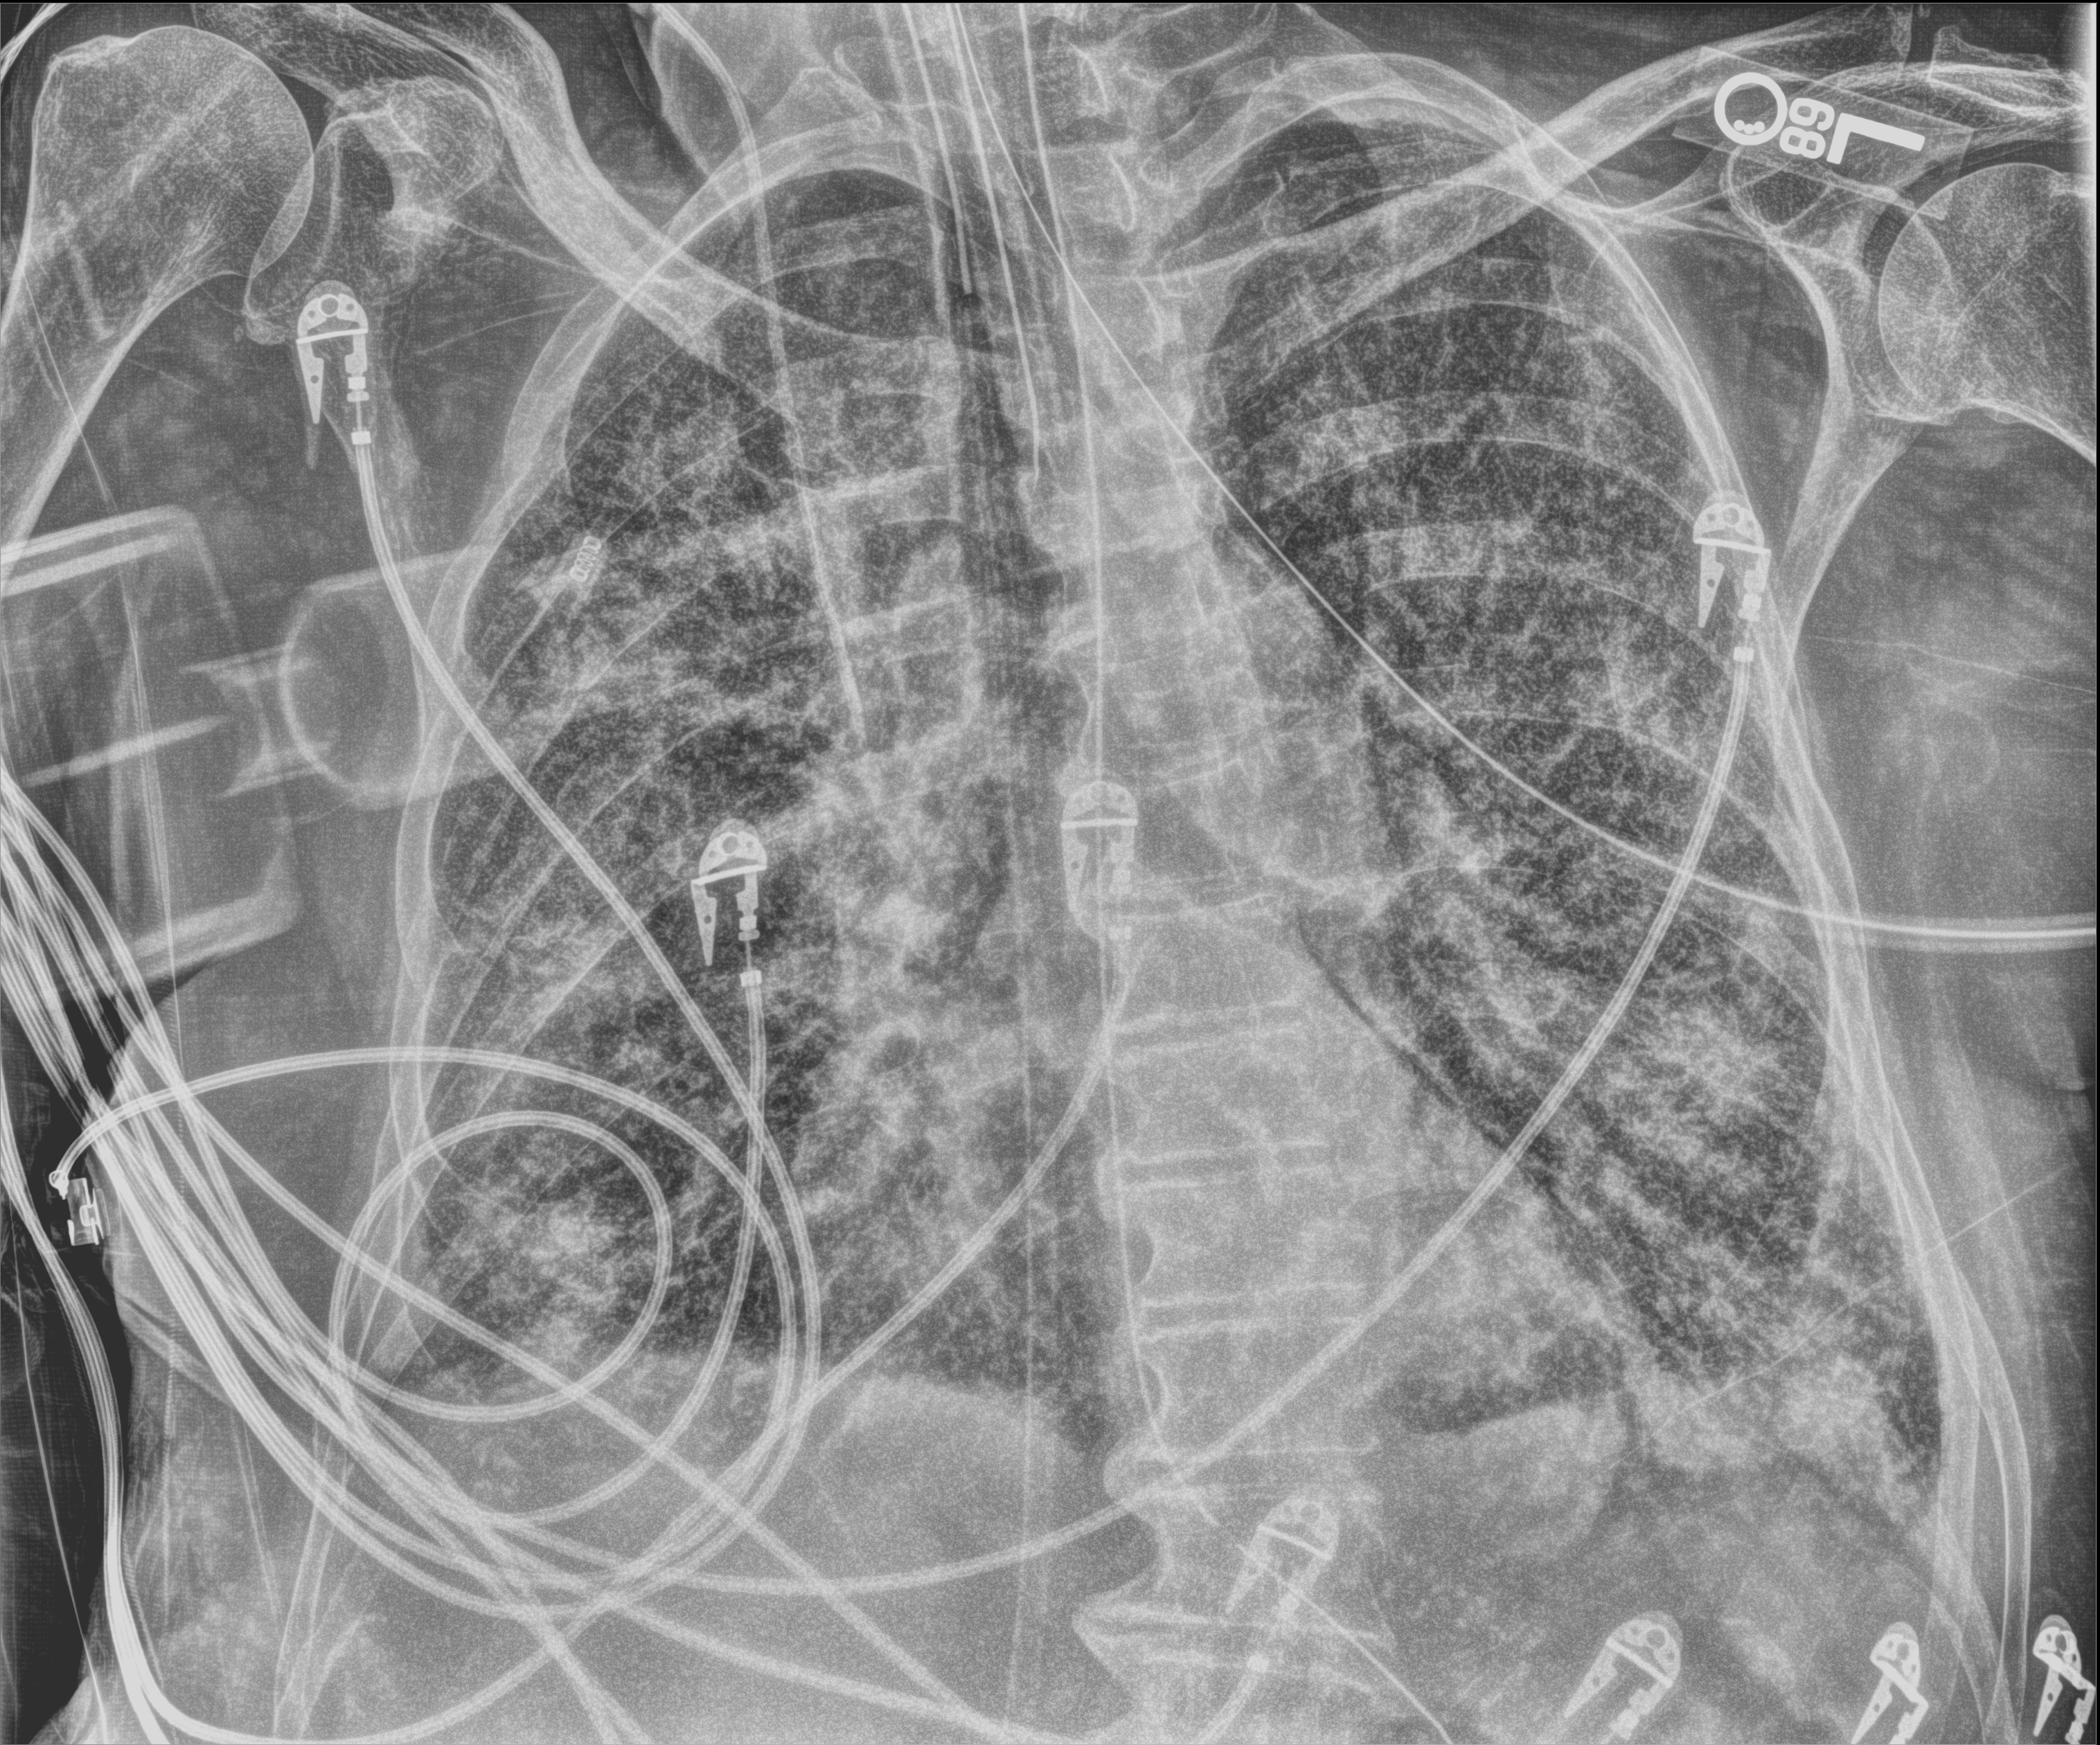
Bedside chest radiograph (digital radiography); anteroposterior (AP) projection. Male patient hospitalised with COVID-19, age 75–90 years.
From the hospital-stay record, not from the radiograph (when in the stay this image was taken is not recorded): COPD (admission record): no; admitted to intensive care during this hospital stay: yes.